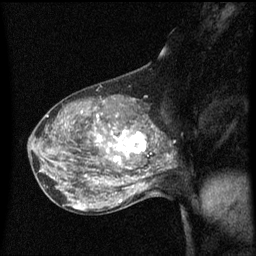
Breast MRI (dynamic contrast-enhanced), one sagittal slice. Position 34 of 60 along the scan axis. Dynamic contrast-enhanced series, image 2 of 3 at this slice position (ordered by acquisition). 1.5 T. TE 4.2 ms, TR 8.4 ms. 2 mm slice thickness. 256 × 256 image matrix, field of view 200 × 200 mm. Female patient, age 50 years.
Outlined on this slice (semi-automatic segmentation, software-assisted and operator-edited):
- analysis volume of interest (the breast-tissue region the enhancement analysis was run in; not a lesion): bounding box [x1, y1, x2, y2] px = [100, 114, 153, 171]
- tumour enhancement mask (voxels above the 70 % enhancement threshold inside the analysis volume of interest): [100, 130, 146, 169]